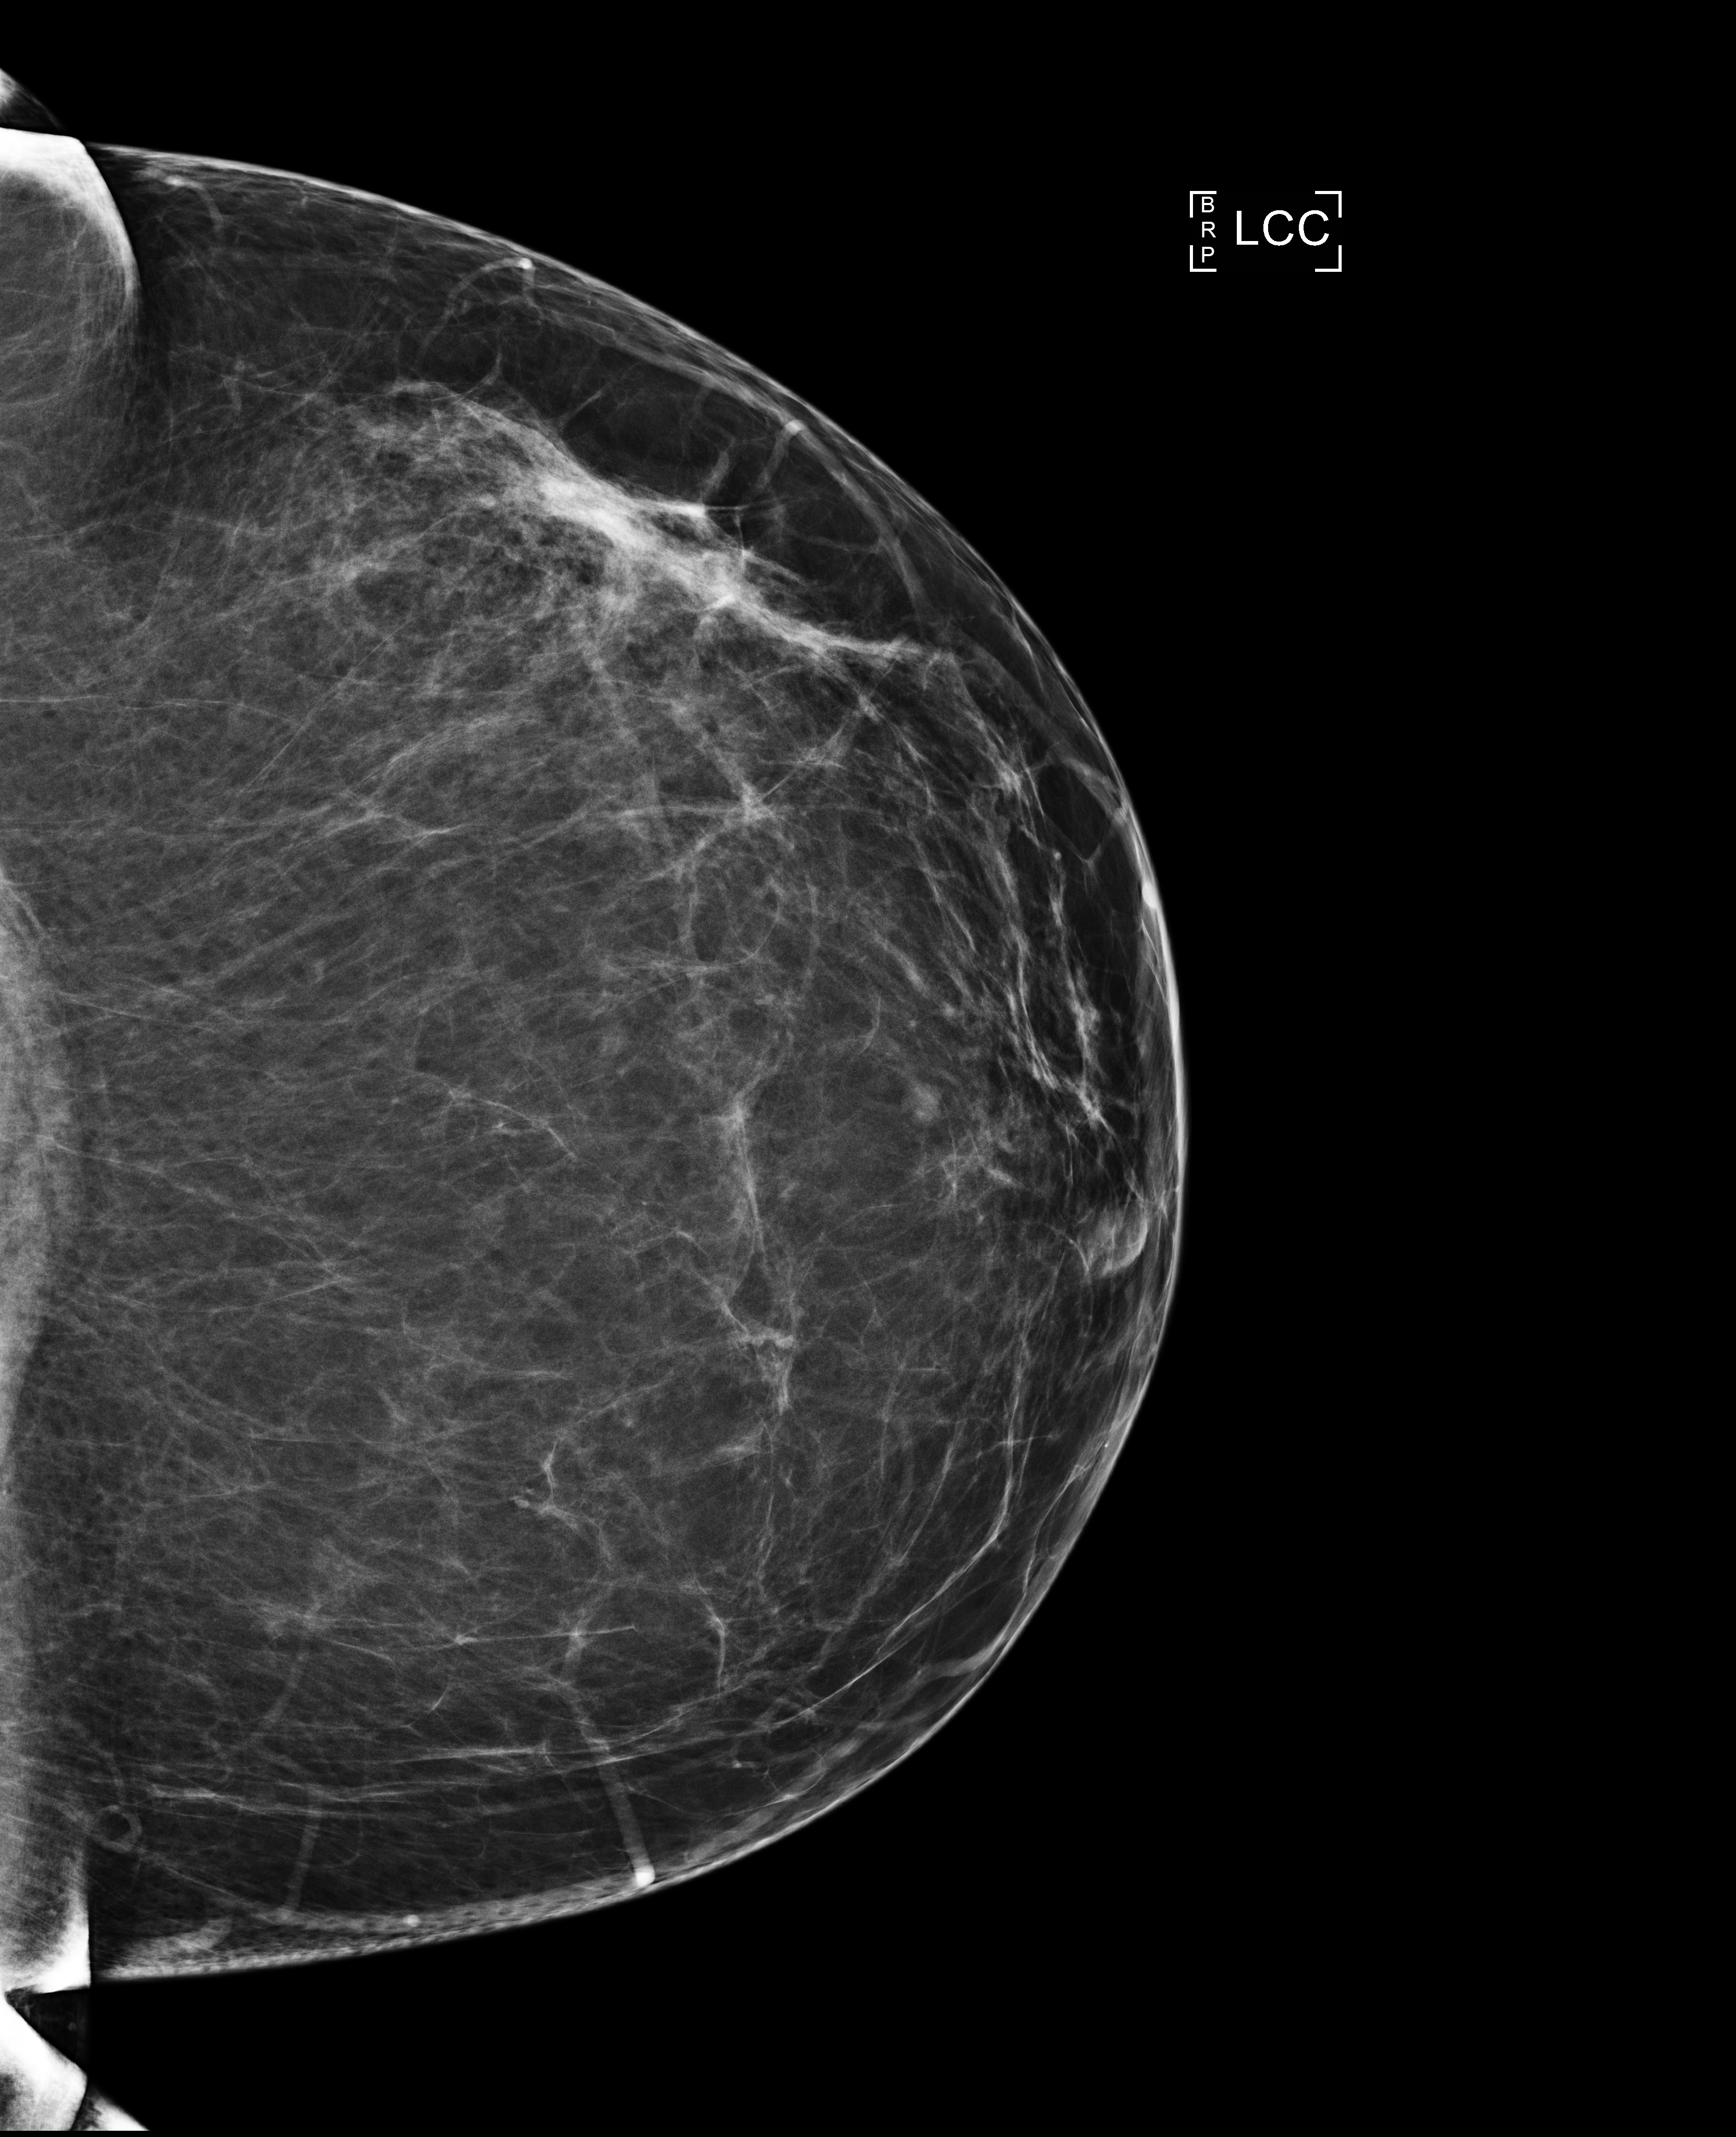
Annual screening mammography examination, compressed breast thickness 86 mm. Female patient, age 51 years.
Image type: full-field digital mammogram. Breast: left. Projection: CC view.